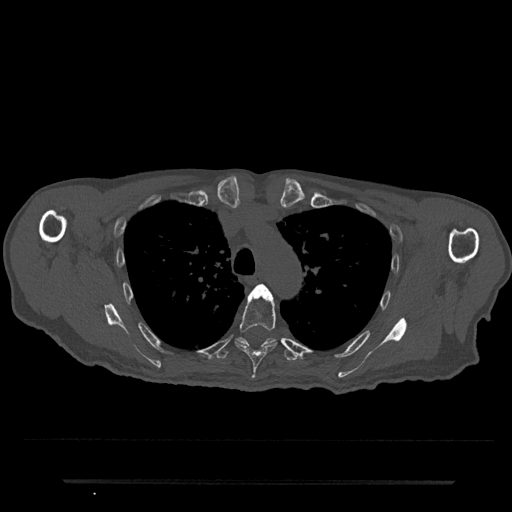
CT including the spine, one axial slice. Position 569 of 797 along the scan axis. Reconstruction kernel Br40s/3. Bone window (W 1800 / L 400 HU). 0.5 mm slice thickness. 512 × 512 image matrix. Patient: male, 74 years. From the clinical record (not read from this slice): primary cancer: prostate.
Annotated regions visible in this slice (semi-automatic segmentation, software-assisted and operator-edited):
- T4 vertebra: bounding box [x1, y1, x2, y2] px = [256, 284, 265, 289]
- T5 vertebra: [235, 284, 277, 379]
- T6 vertebra: [215, 337, 298, 361]